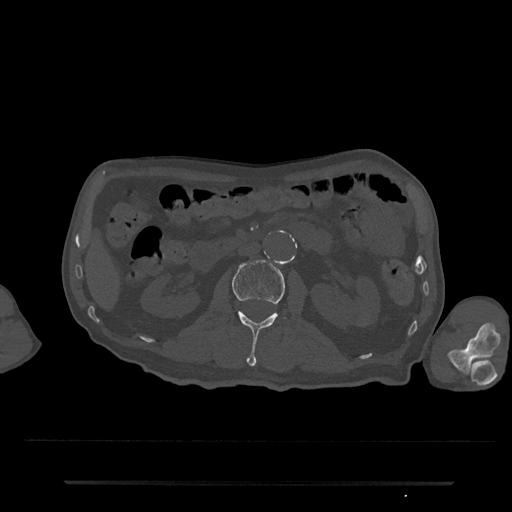
CT including the spine, one axial slice; slice 54 of 797 in the series (ordered by position); 120 kVp; bone window (W 1800 / L 400 HU); 0.5 mm slice thickness; 512 × 512 image matrix, field of view 427 × 427 mm. Patient: male, 74 years. From the clinical record (not read from this slice): primary cancer: prostate.
Structures marked on this image (semi-automatically segmented with operator editing):
- L2 vertebra: bounding box (x1, y1, x2, y2) in pixels: (233, 260, 287, 366)